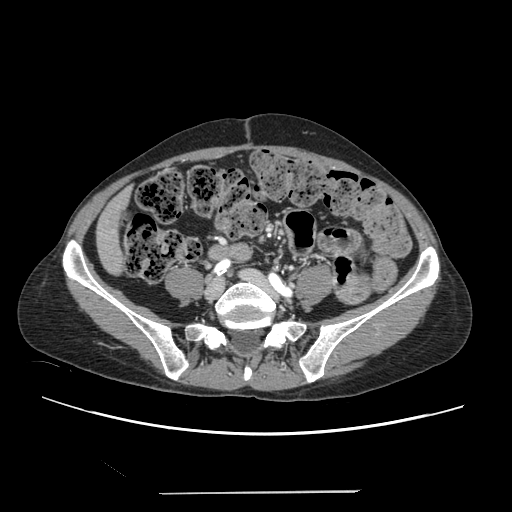
Contrast-enhanced abdominal CT, one axial slice; position 17 of 240 along the scan axis; 120 kVp; intravenous contrast given; soft-tissue window (W 400 / L 40 HU); 1.25 mm slice thickness; 512 × 512 image matrix, field of view 371 × 371 mm. Female patient, age 60 years. From the clinical record (not read from this slice): diagnosis: colorectal cancer liver metastases, imaged before liver resection; multiple liver metastases: no; largest metastasis: 1.5 cm; disease in both lobes: no.
Structures marked on this image (outlined manually by an expert reader):
- liver: bounding box (x1, y1, x2, y2) in pixels: (98, 193, 129, 273)
- planned liver remnant (the part of the liver to remain after resection): (98, 193, 128, 273)